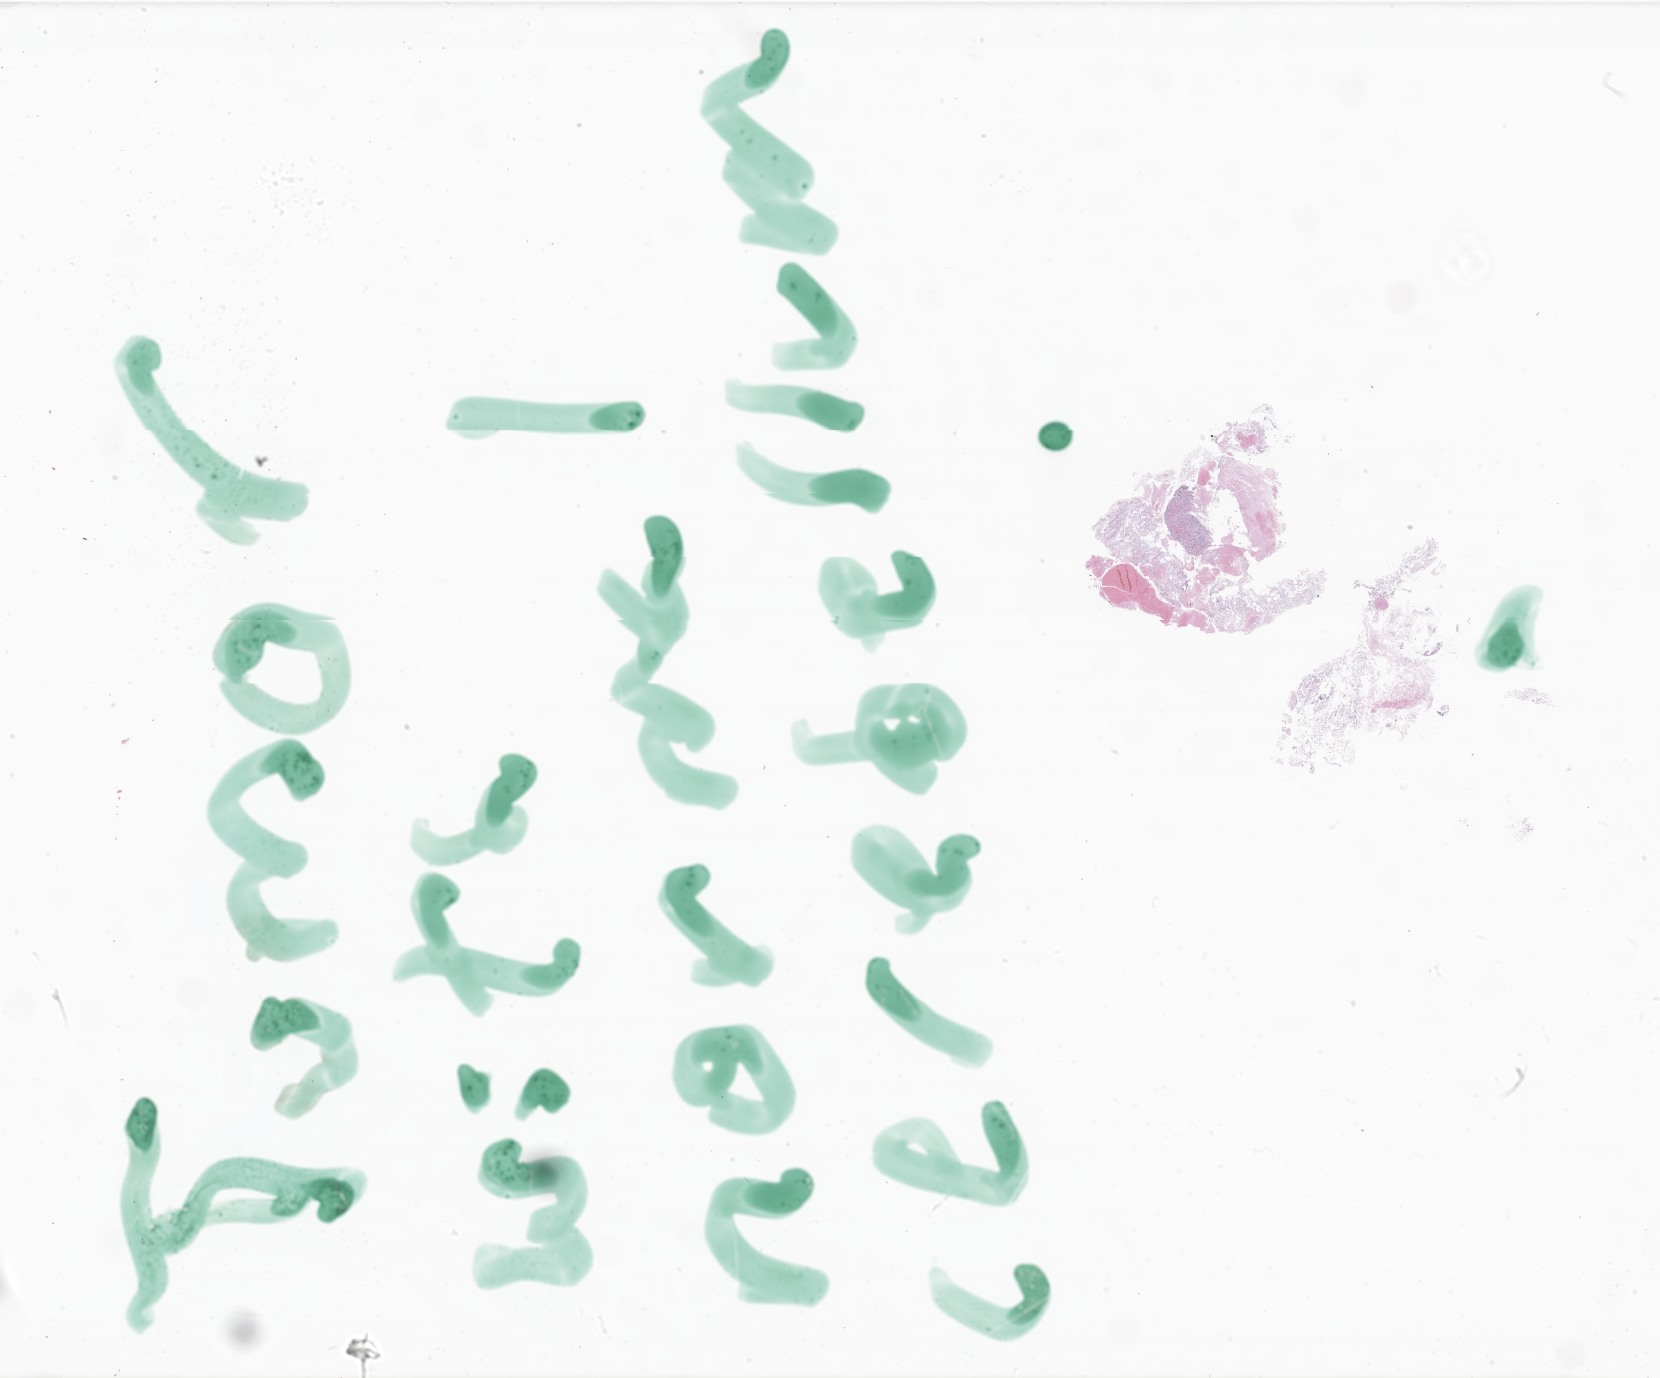
Whole-slide image, haematoxylin and eosin stain of tumor tissue from the brain stem — whole scanned area (about 28.0 x 23.2 mm) shown as a low-resolution overview. Formalin-fixed, paraffin-embedded (FFPE) tissue. Male patient, age 143 months (11 years 11 months).
* recorded diagnosis: Glioma, malignant